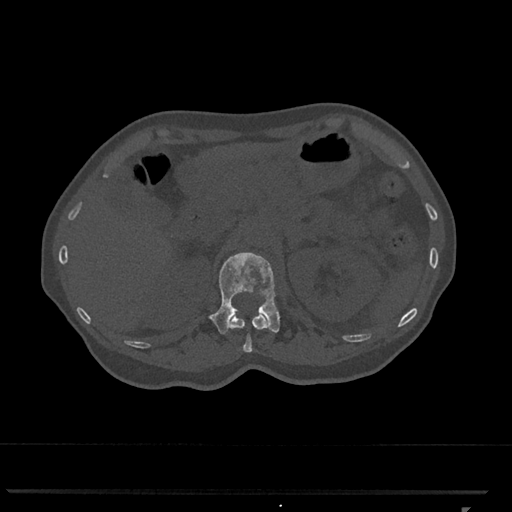
CT including the spine, one axial slice; position 423 of 793 along the scan axis; reconstruction kernel Br40s/3; 120 kVp; bone window (W 1800 / L 400 HU); 0.5 mm slice thickness; 512 × 512 image matrix, field of view 380 × 380 mm. Female patient, age 62 years. From the clinical record (not read from this slice): primary cancer: renal.
Structures marked on this image (semi-automatically segmented with operator editing):
- L1 vertebra: box from (x=208, y=252) to (x=280, y=334) px
- T12 vertebra: (x=230, y=312)–(x=267, y=353)